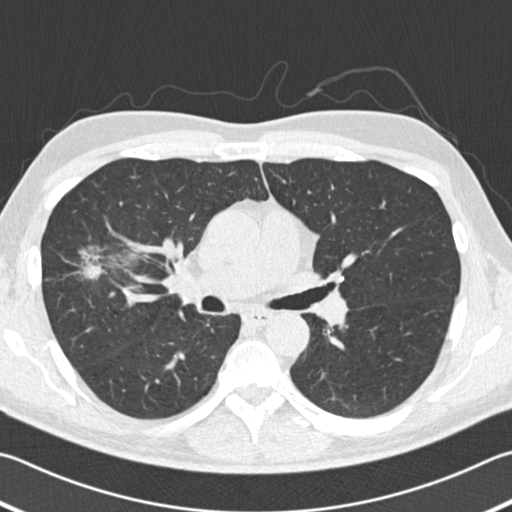
Chest CT (low-dose screening protocol), one axial image, second annual screen, lung window (W 1500 / L -600 HU), standard (soft-tissue) reconstruction kernel (B30f), slice 71 of 182 in the series, 512 × 512 image matrix, field of view 344 × 344 mm. Male, age 56 years at enrolment. Former smoker at enrolment.
Expert-annotated lung lesion, bounding box (x1, y1, x2, y2) in pixels: (51, 234, 140, 299). Reader record for this screening exam (exam-level; its link to the box is not recorded): non-calcified nodule or mass ≥4 mm, right upper lobe, 18 × 14 mm, spiculated (stellate) margins, soft tissue attenuation, pre-existing on the prior screen: yes; interval growth: yes. Official screen result: positive, other. Later outcome: lung cancer diagnosed 42 days after this screen — bronchiolo-alveolar adenocarcinoma, NOS, right upper lobe, well differentiated (G1), stage IIB (AJCC 6th edition), 30 mm at pathology.